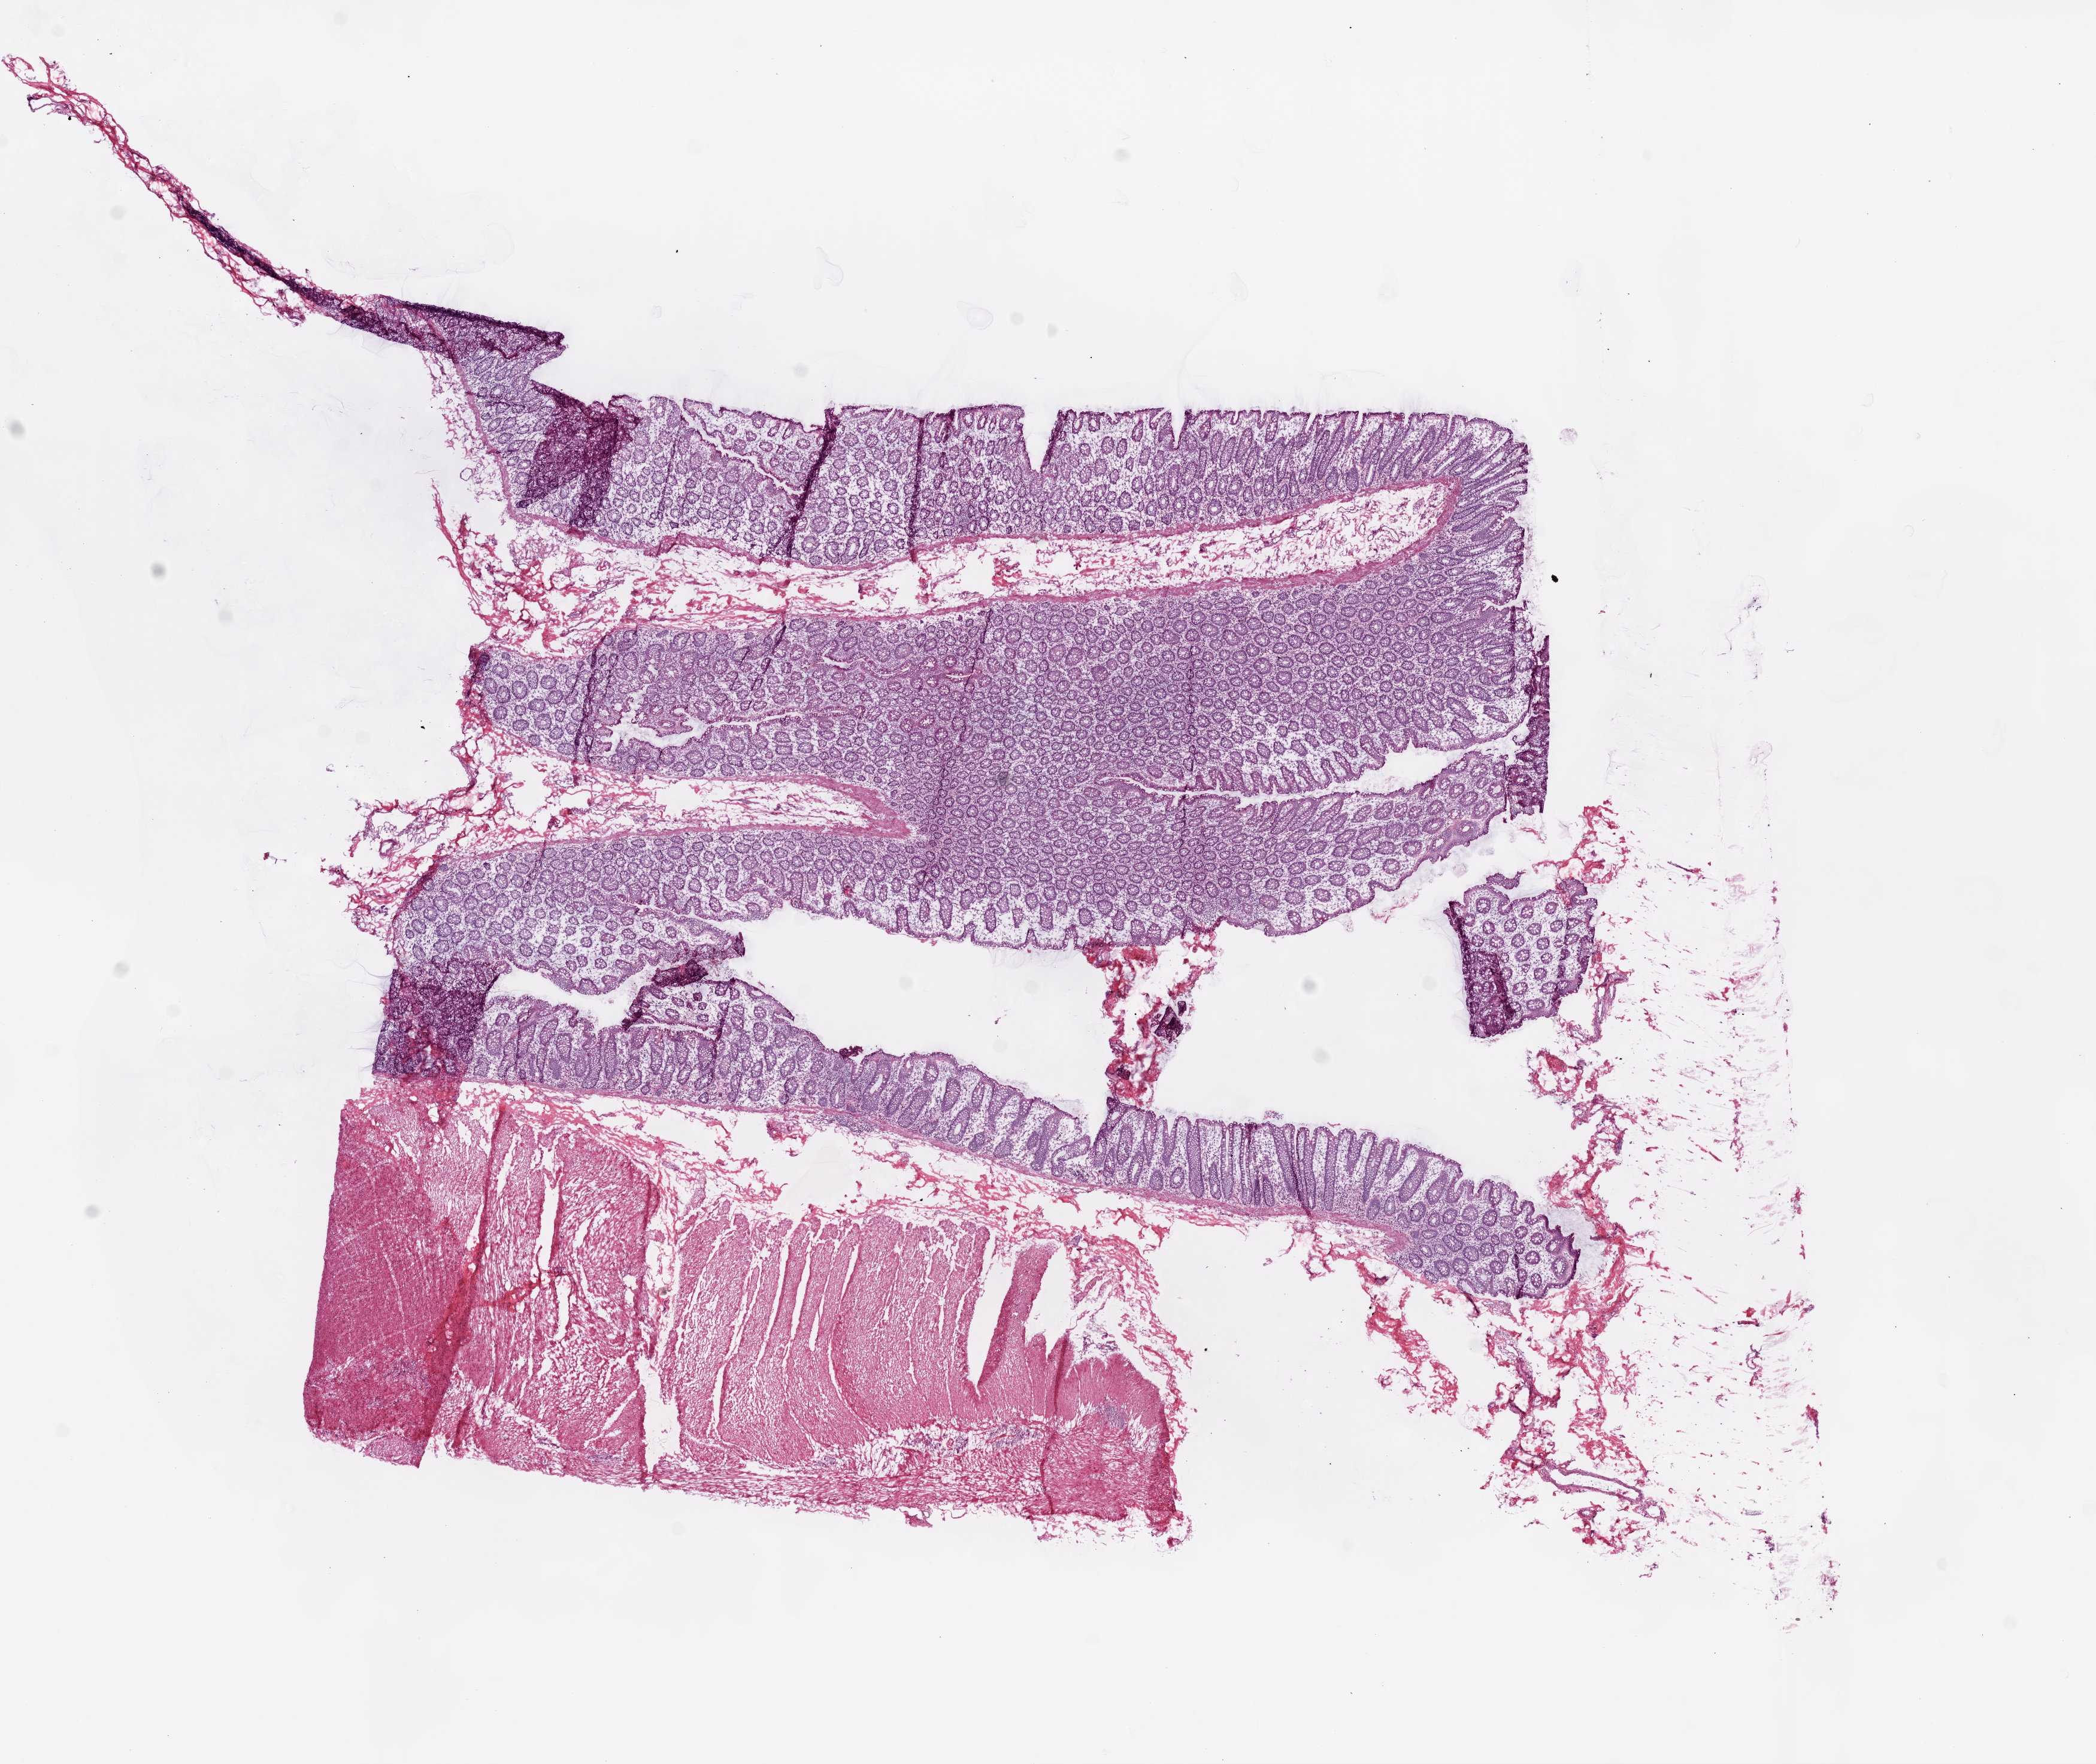
Whole-slide histology image, H&E-stained — a low-resolution overview of the entire scanned area, about 14.0 x 11.8 mm (acquisition: 20x scan); frozen section; solid tissue normal (non-tumour tissue) sample from the colon. Male, age 79 years at initial diagnosis.
This section: solid tissue normal (non-tumour) sample from the same patient. Patient diagnosis: Adenocarcinoma, NOS (ascending colon).